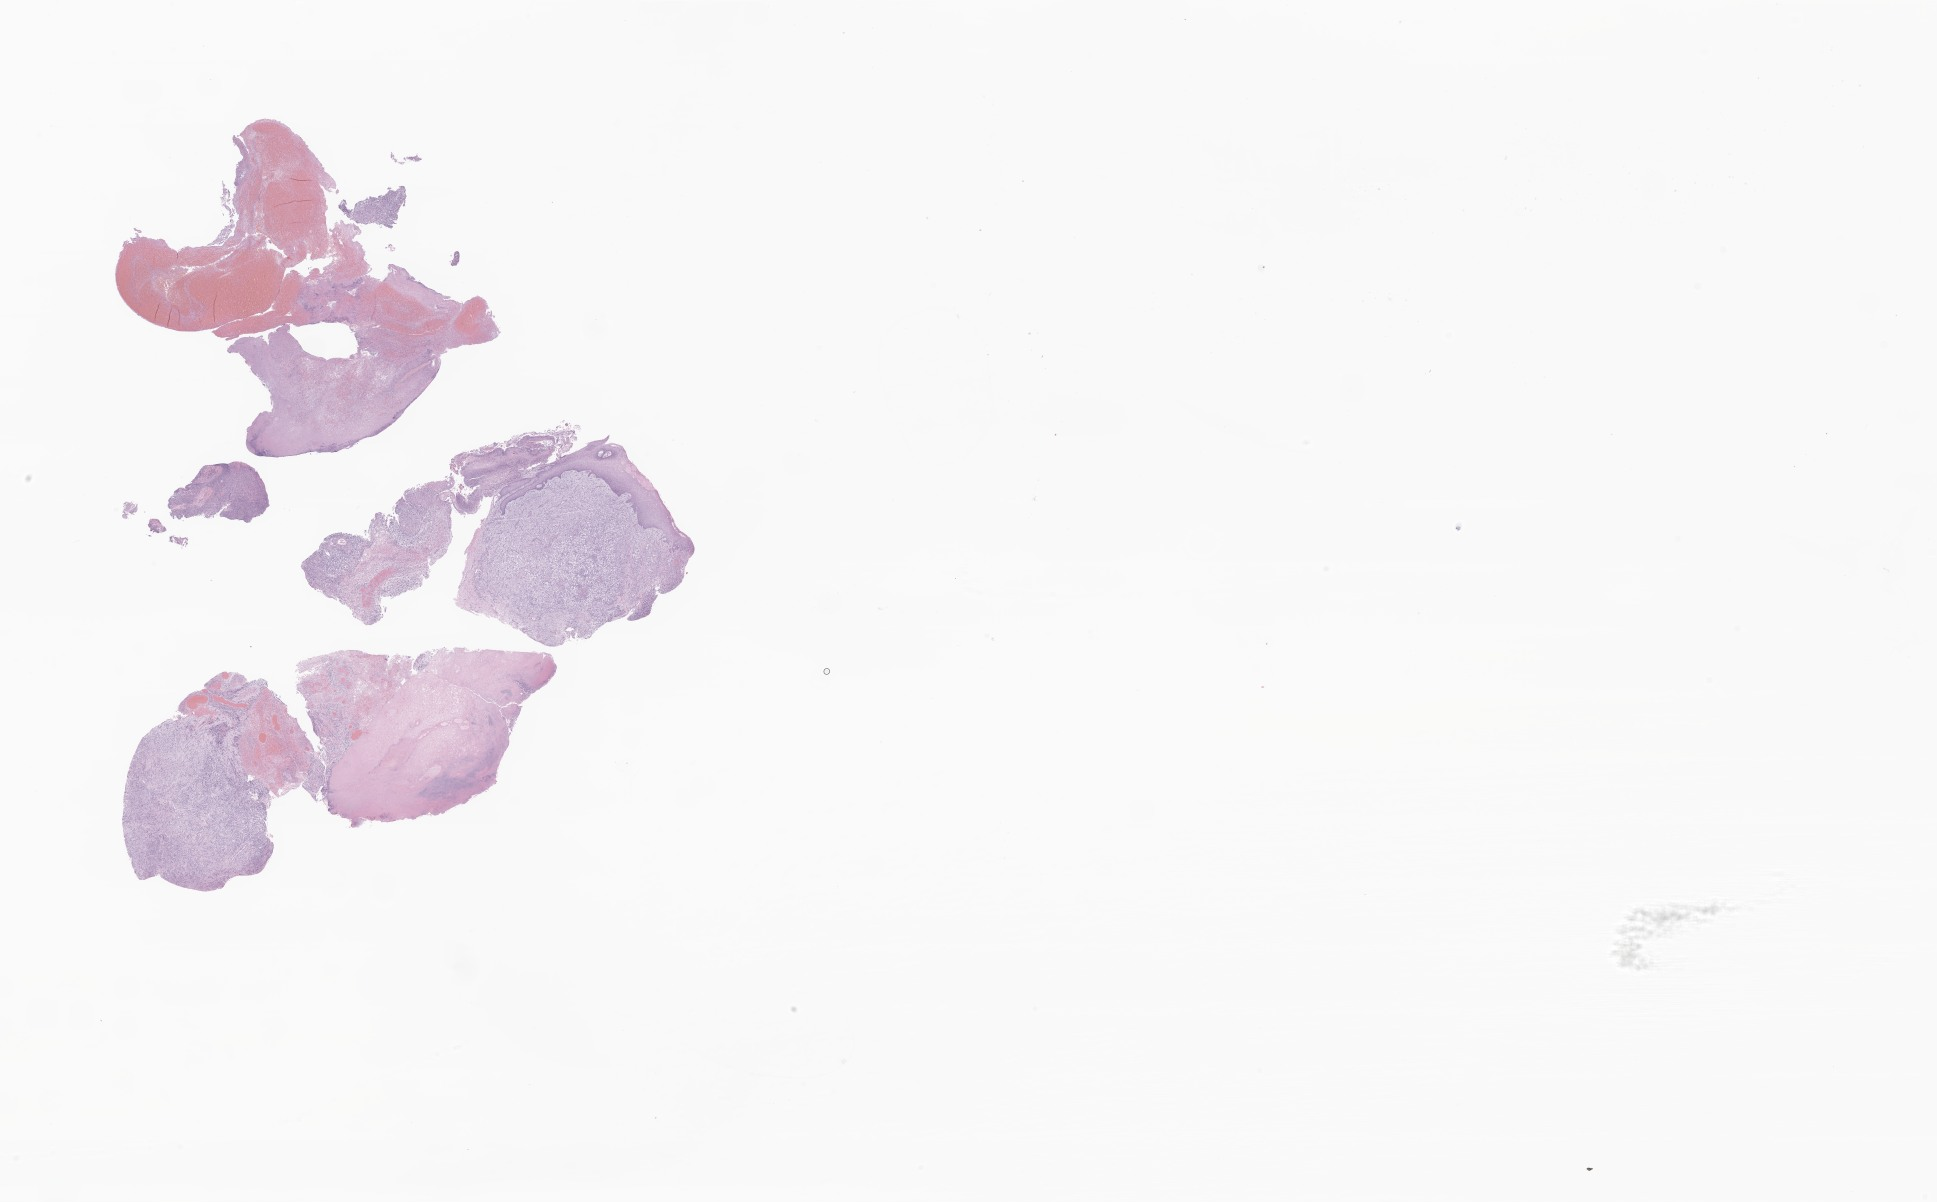
Whole-slide image, haematoxylin and eosin stain of tumor tissue from the posterior wall of oropharynx, a low-resolution overview of the entire scanned area, about 32.7 x 20.3 mm. Formalin-fixed paraffin-embedded section. Patient: male, age 231 months (19 years 3 months).
Recorded diagnosis: Embryonal rhabdomyosarcoma, NOS.